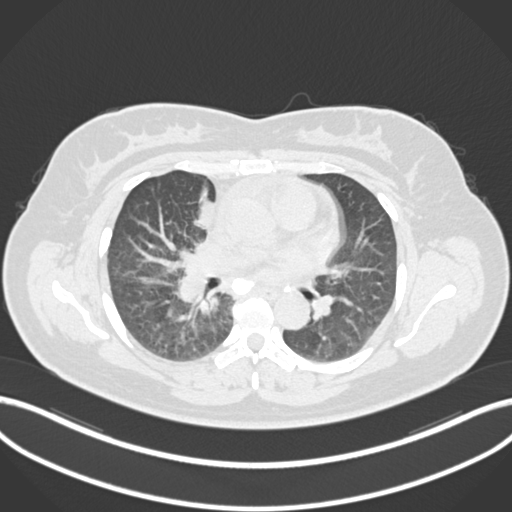
Chest CT, one axial slice; slice 90 of 183 in the series (ordered by position); reconstruction kernel B30f; 120 kVp; lung window (W 1500 / L -600 HU); 512 × 512 image matrix. Patient: female, 46 years. Case-level facts recorded for this patient, not image findings: clinical TNM (as recorded): T2a N1 M0.
Outlined on this slice (bounding box drawn by a radiologist):
- lung tumour (recorded histology: adenocarcinoma): bounding box (x1, y1, x2, y2) in pixels: (189, 195, 219, 233)